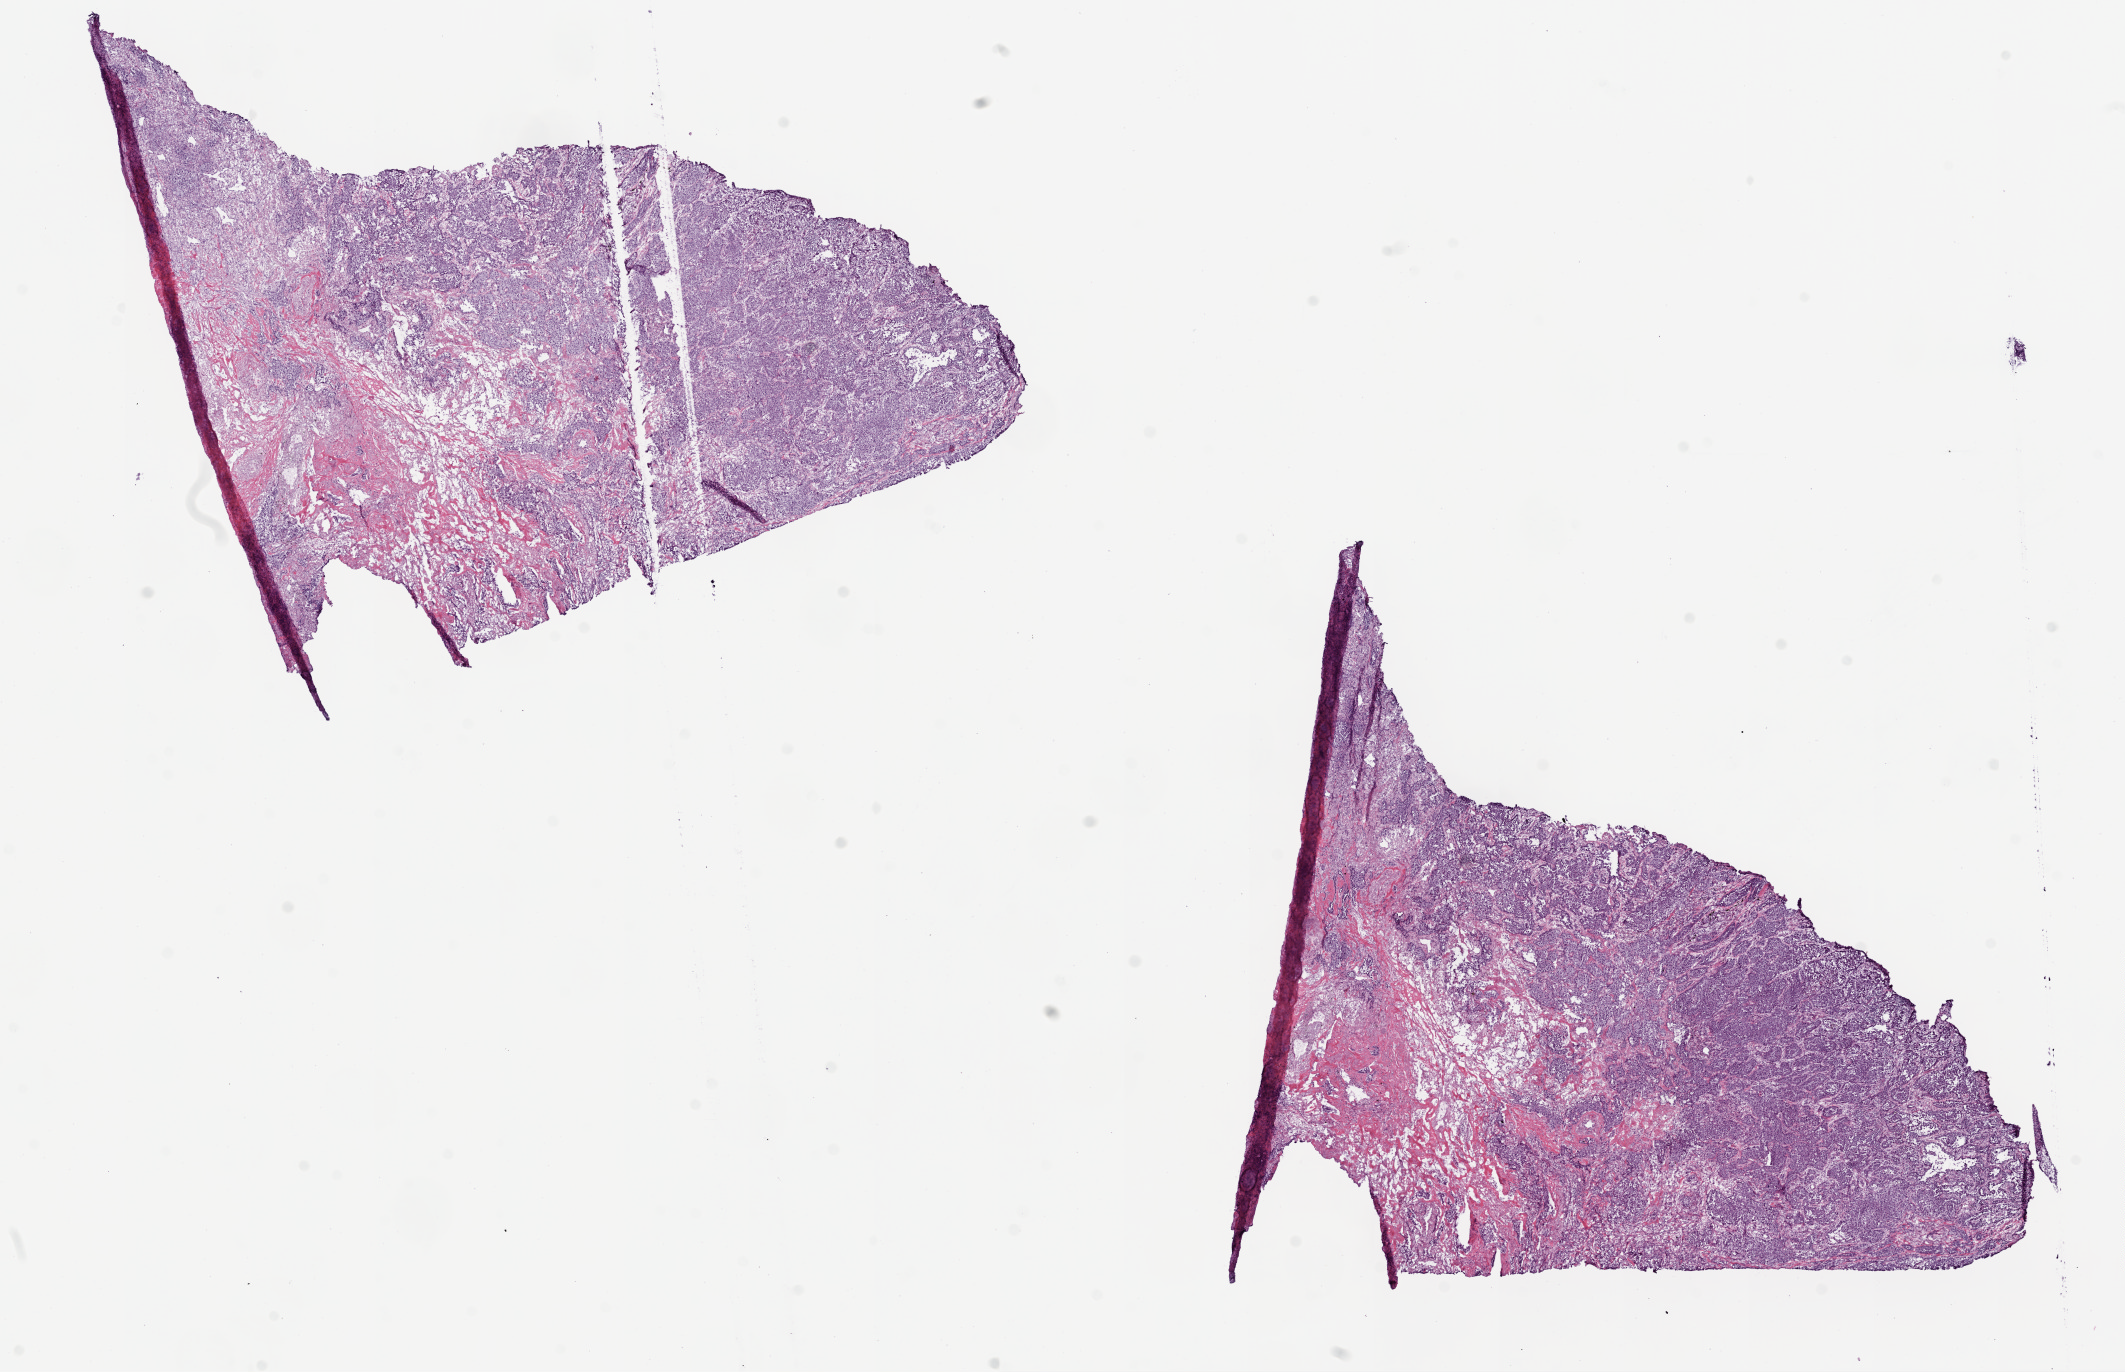
H&E whole-slide image, shown as a low-resolution overview of the whole scanned area (about 17.1 x 11.0 mm, from a 20x scan); frozen section; primary tumour sample from the lung. Male, age 57 years at initial diagnosis. Slide review estimates, as recorded: tumour cells 70%, tumour nuclei 75%.
Histologic diagnosis: Adenocarcinoma with mixed subtypes.